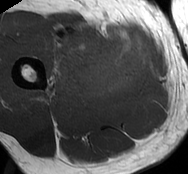
MRI of an extremity soft-tissue mass, one axial slice; slice 29 of 93 in the series (ordered by position); MR volume resampled by the dataset authors to the PET/CT grid (not the native acquisition matrix); 188 × 174 image matrix. Male patient. Case-level facts recorded for this patient, not image findings: histological type: undifferentiated - pleiomorphic; grade: high; site of the primary tumour: right thigh.
Outlined on this slice (expert contour drawn on MRI and transferred to this co-registered scan by the dataset authors):
- gross tumour volume including surrounding oedema: bounding box [x1, y1, x2, y2] px = [45, 28, 149, 102]
- gross tumour volume (mass): [79, 33, 149, 98]